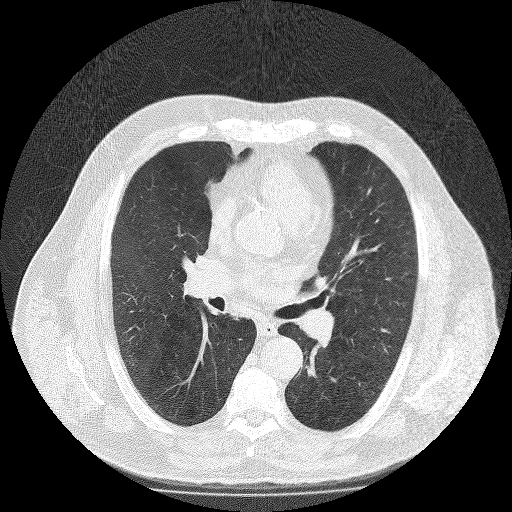
Low-dose screening chest CT, axial slice. Second screening round (one year after baseline). Lung window (W 1500 / L -600 HU). 2 mm slice thickness. 120 kVp. Male, age 65 years at enrolment. Former smoker at enrolment.
Expert-annotated lung lesion, bounding box [x1, y1, x2, y2] px = [212, 302, 255, 332]. The exam's reader record, not a measurement of the box and not confirmed to be the same lesion: non-calcified nodule or mass ≥4 mm, right lower lobe, 10 × 9 mm, spiculated (stellate) margins, soft tissue attenuation, pre-existing on the prior screen: yes; interval growth: no.